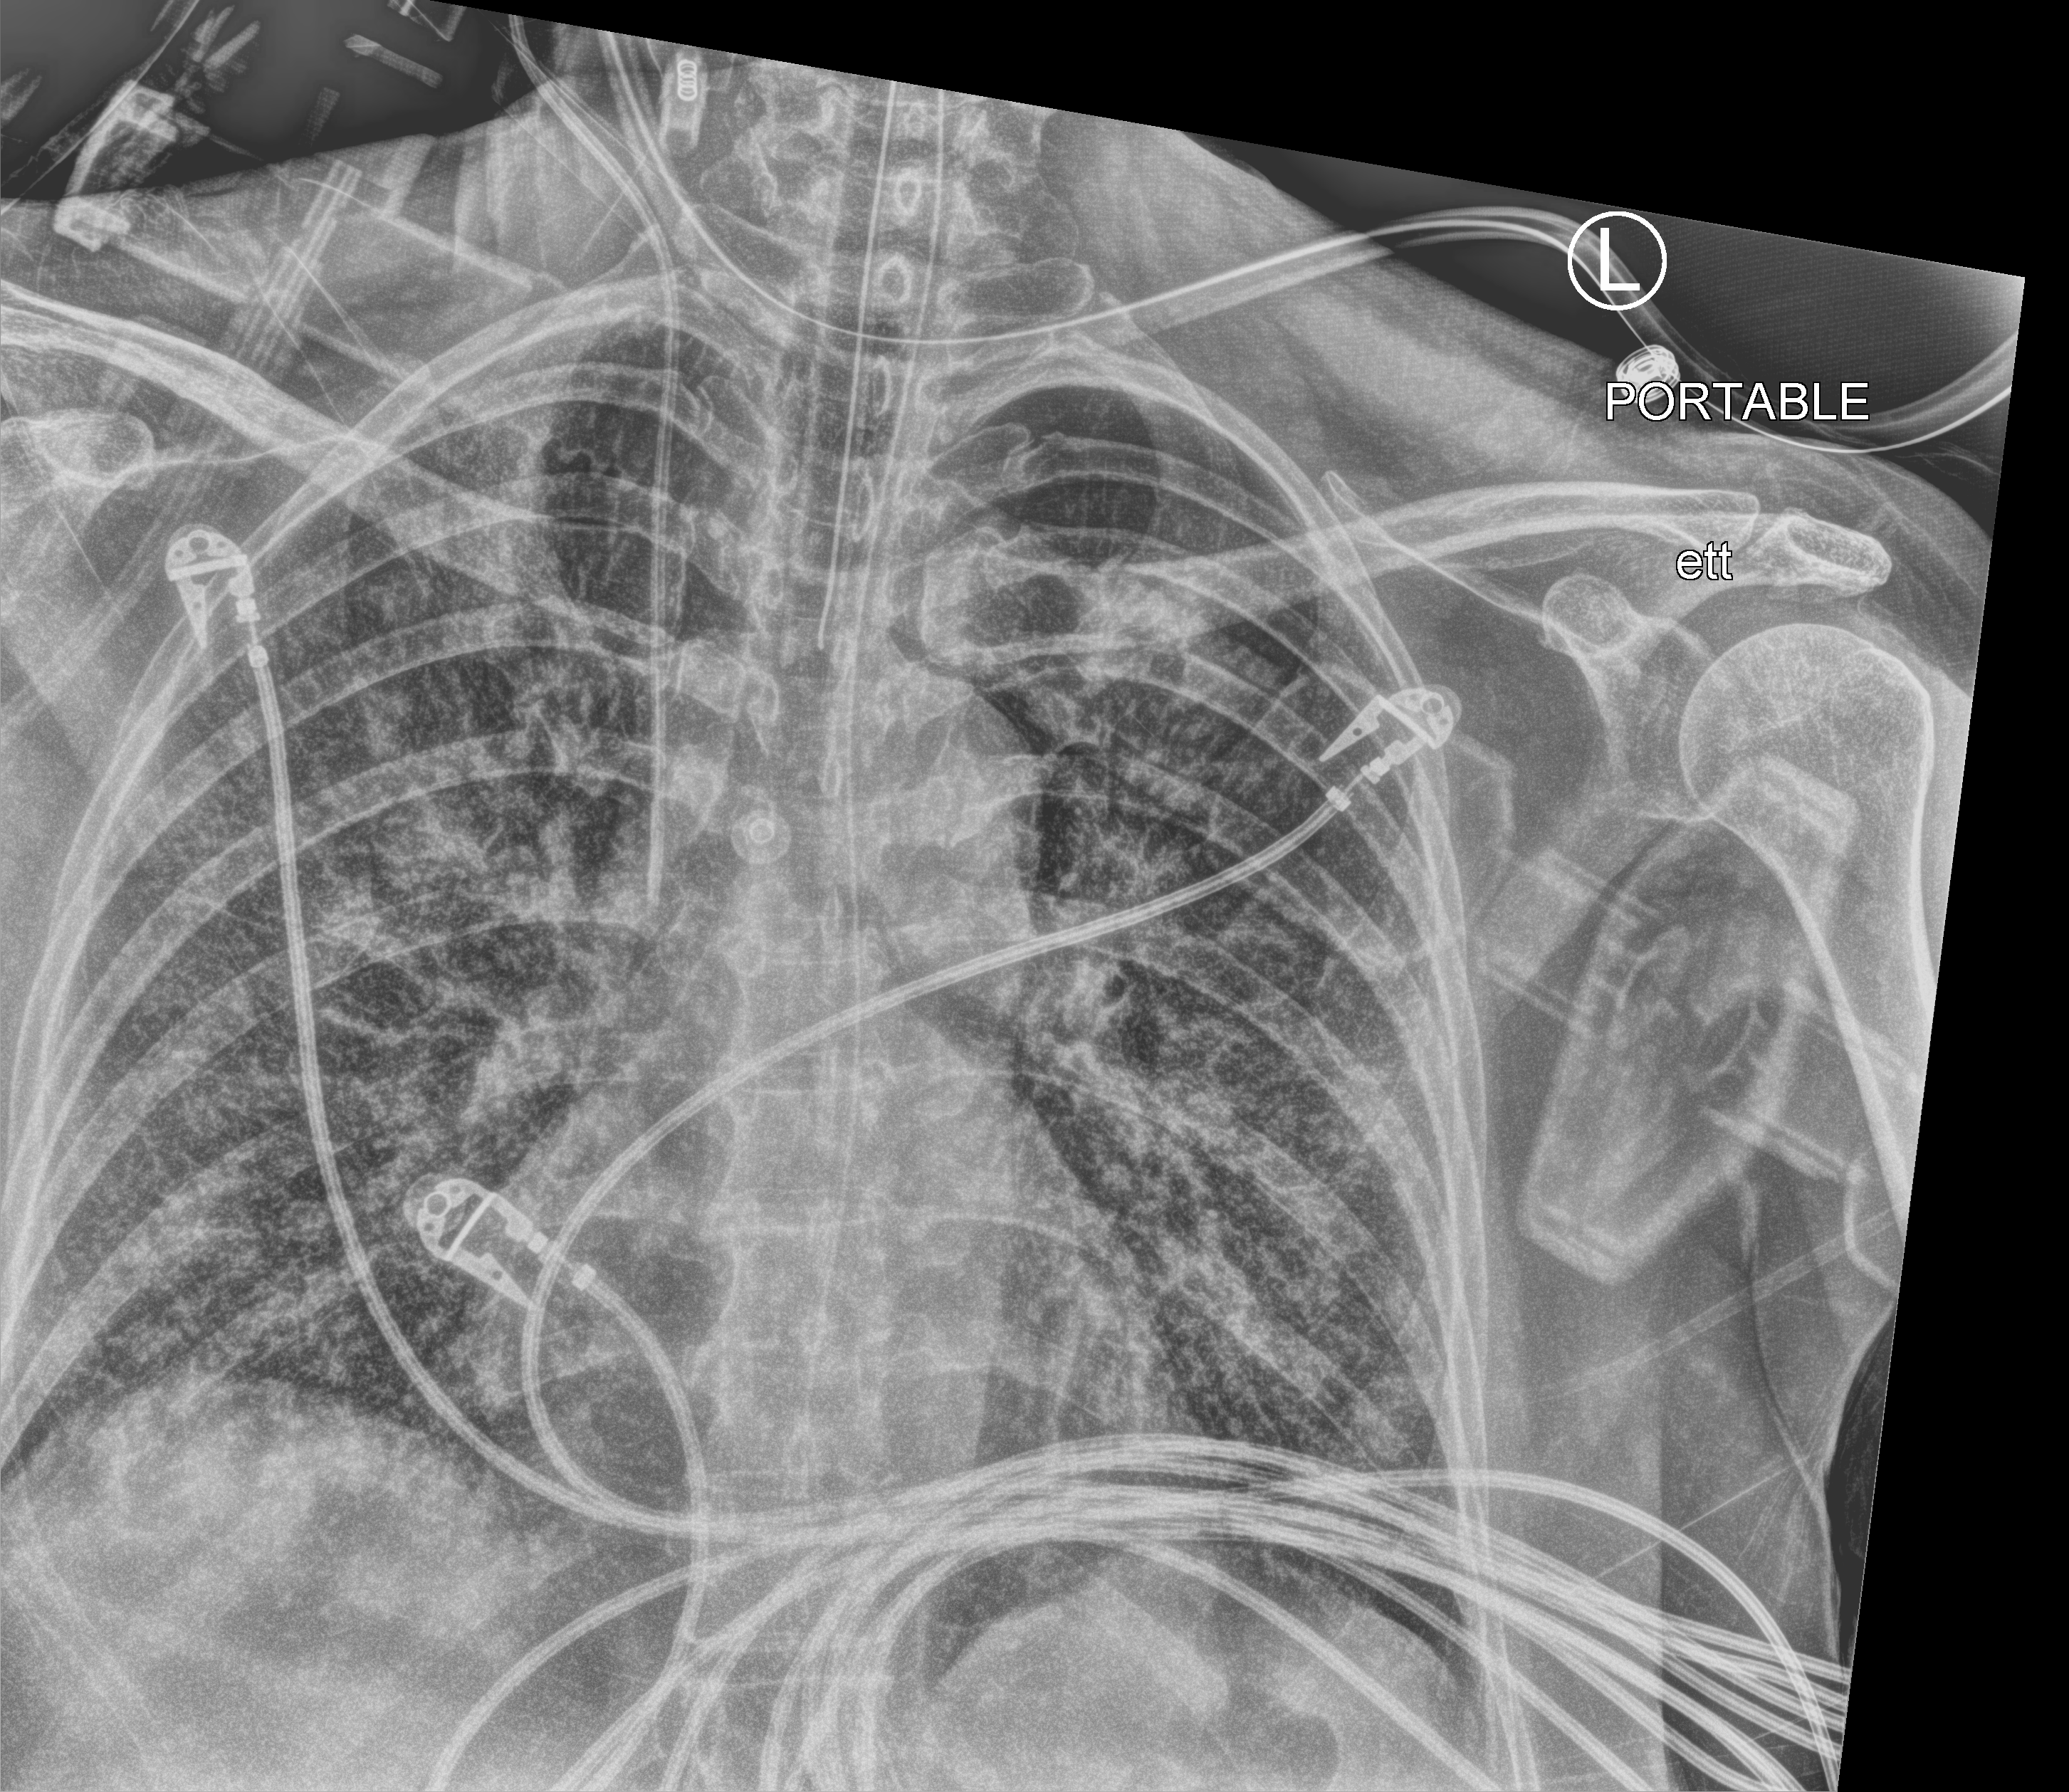
Portable chest radiograph; anteroposterior (AP) projection. Female patient hospitalised with COVID-19, age 60–74 years.
Hospital-stay facts (about this admission, not read from this image; timing relative to this image not recorded):
- mechanically ventilated during this hospital stay: yes
- chronic kidney disease (admission record): no
- length of hospital stay: 43 days